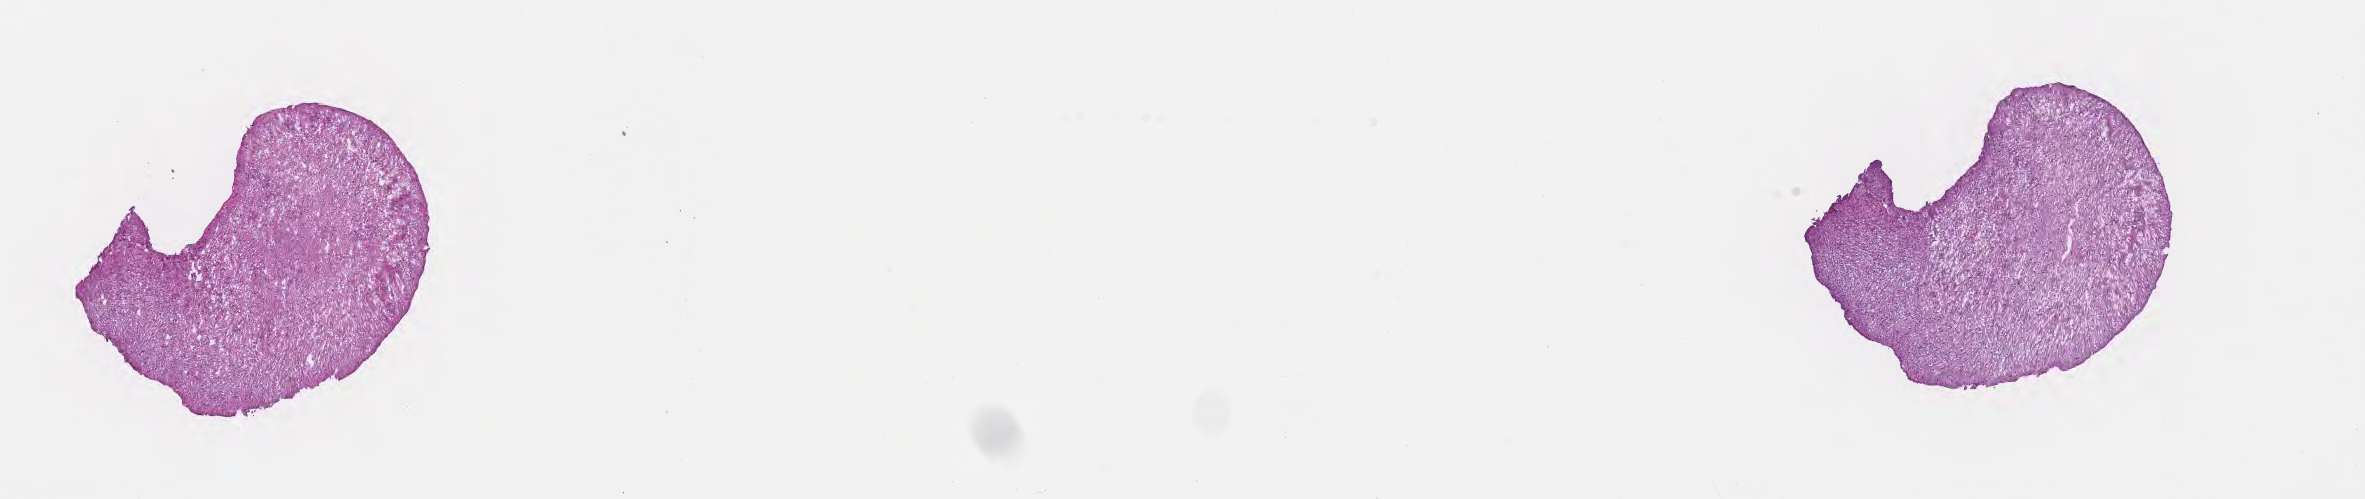
H&E whole-slide image — shown as a low-resolution overview of the whole scanned area (about 19.1 x 4.0 mm); frozen section (tissue freezing medium); specimen: recurrent tumor; anatomic site: brain. Male, age 52 years at initial diagnosis. Composition of this section per pathologist review: tumor cells 42%, tumor nuclei 63%, stromal cells 33%, necrosis 0%, normal cells 25%. Inflammatory infiltration, as recorded: lymphocyte infiltration 0%, monocyte infiltration 0%, neutrophil infiltration 0%.
Patient diagnosis: Glioblastoma, NOS.